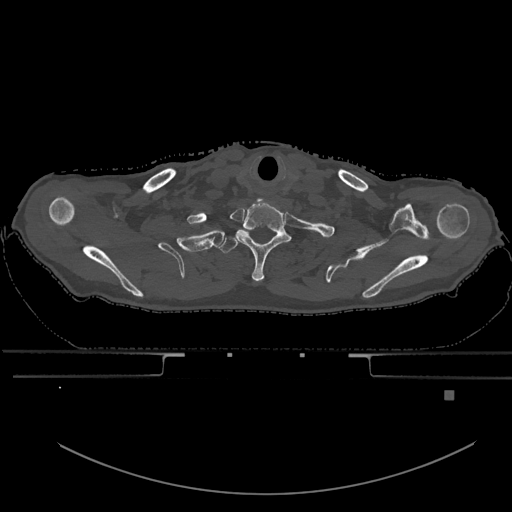
CT including the spine, one axial slice. Bone window (W 1800 / L 400 HU). 0.5 mm slice thickness. 512 × 512 image matrix, field of view 456 × 456 mm. Patient: male, 82 years. Case-level facts recorded for this patient, not image findings: primary cancer: prostate.
Structures marked on this image (semi-automatic segmentation, software-assisted and operator-edited):
- T1 vertebra: bounding box (x1, y1, x2, y2) in pixels: (219, 237, 299, 254)